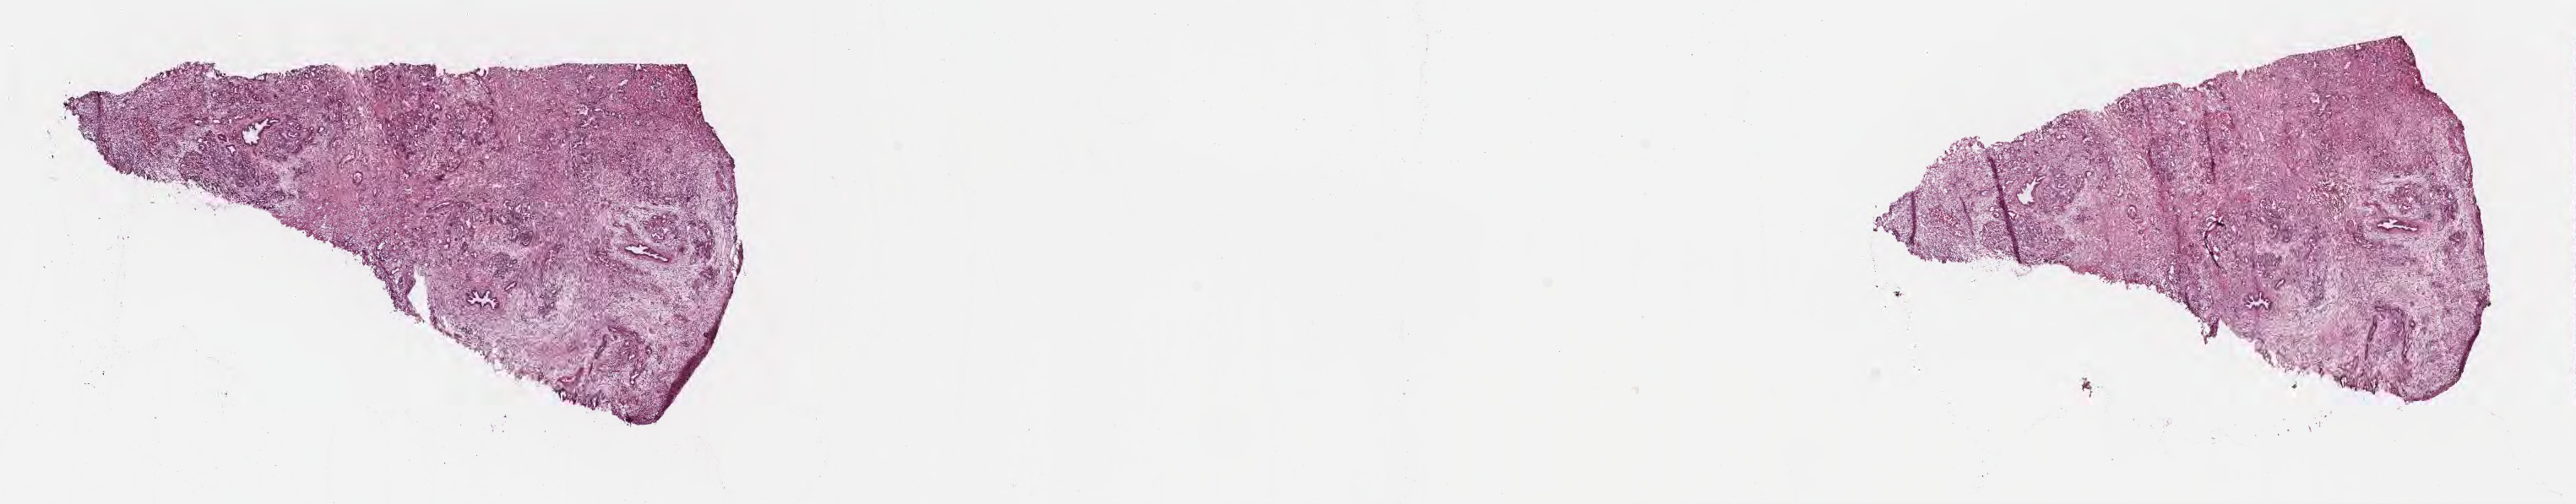
Whole-slide image, H&E stain — whole scanned area (about 24.7 x 4.8 mm) shown as a low-resolution overview. Frozen section. Specimen: primary tumor. Site: head of pancreas. Female, age 60 years at initial diagnosis. Tumor grade: G2 (moderately differentiated). Composition of this section per pathologist review: tumor cells 50%, tumor nuclei 60%, stromal cells 50%, necrosis 0%, normal cells 0%. Inflammatory infiltration, as recorded: lymphocyte infiltration 0%, monocyte infiltration 0%, neutrophil infiltration 0%.
* AJCC pathologic stage: Stage III
* histologic diagnosis: Infiltrating duct carcinoma, NOS
* section: bottom of the tissue portion